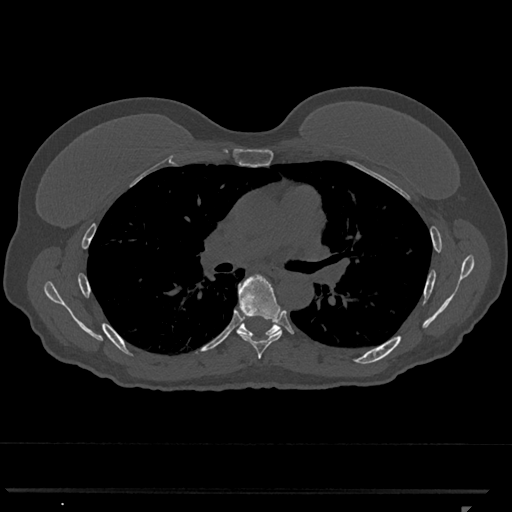
CT including the spine, one axial slice. Slice 744 of 793 in the series (ordered by position). Bone window (W 1800 / L 400 HU). 0.5 mm slice thickness. 512 × 512 image matrix, field of view 380 × 380 mm. Female patient, age 62 years. Case-level facts recorded for this patient, not image findings: primary cancer: renal.
Outlined on this slice (semi-automatically segmented with operator editing):
- T6 vertebra: bounding box [x1, y1, x2, y2] px = [238, 274, 282, 359]
- T7 vertebra: [237, 322, 280, 338]